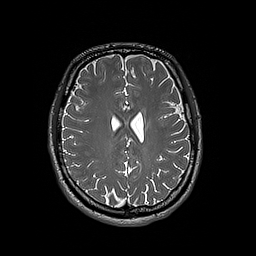
Brain MRI from a brain-tumour surgery series, one axial slice; slice 72 of 192 in the series (ordered by position); 1 mm slice thickness; 256 × 256 image matrix. Case-level facts recorded for this patient, not image findings: histopathology: Oligodendroglioma; WHO grade: 3.
Annotated regions visible in this slice (expert manual segmentation):
- tumour: bounding box <146,122,153,128> (left, top, right, bottom; pixels)